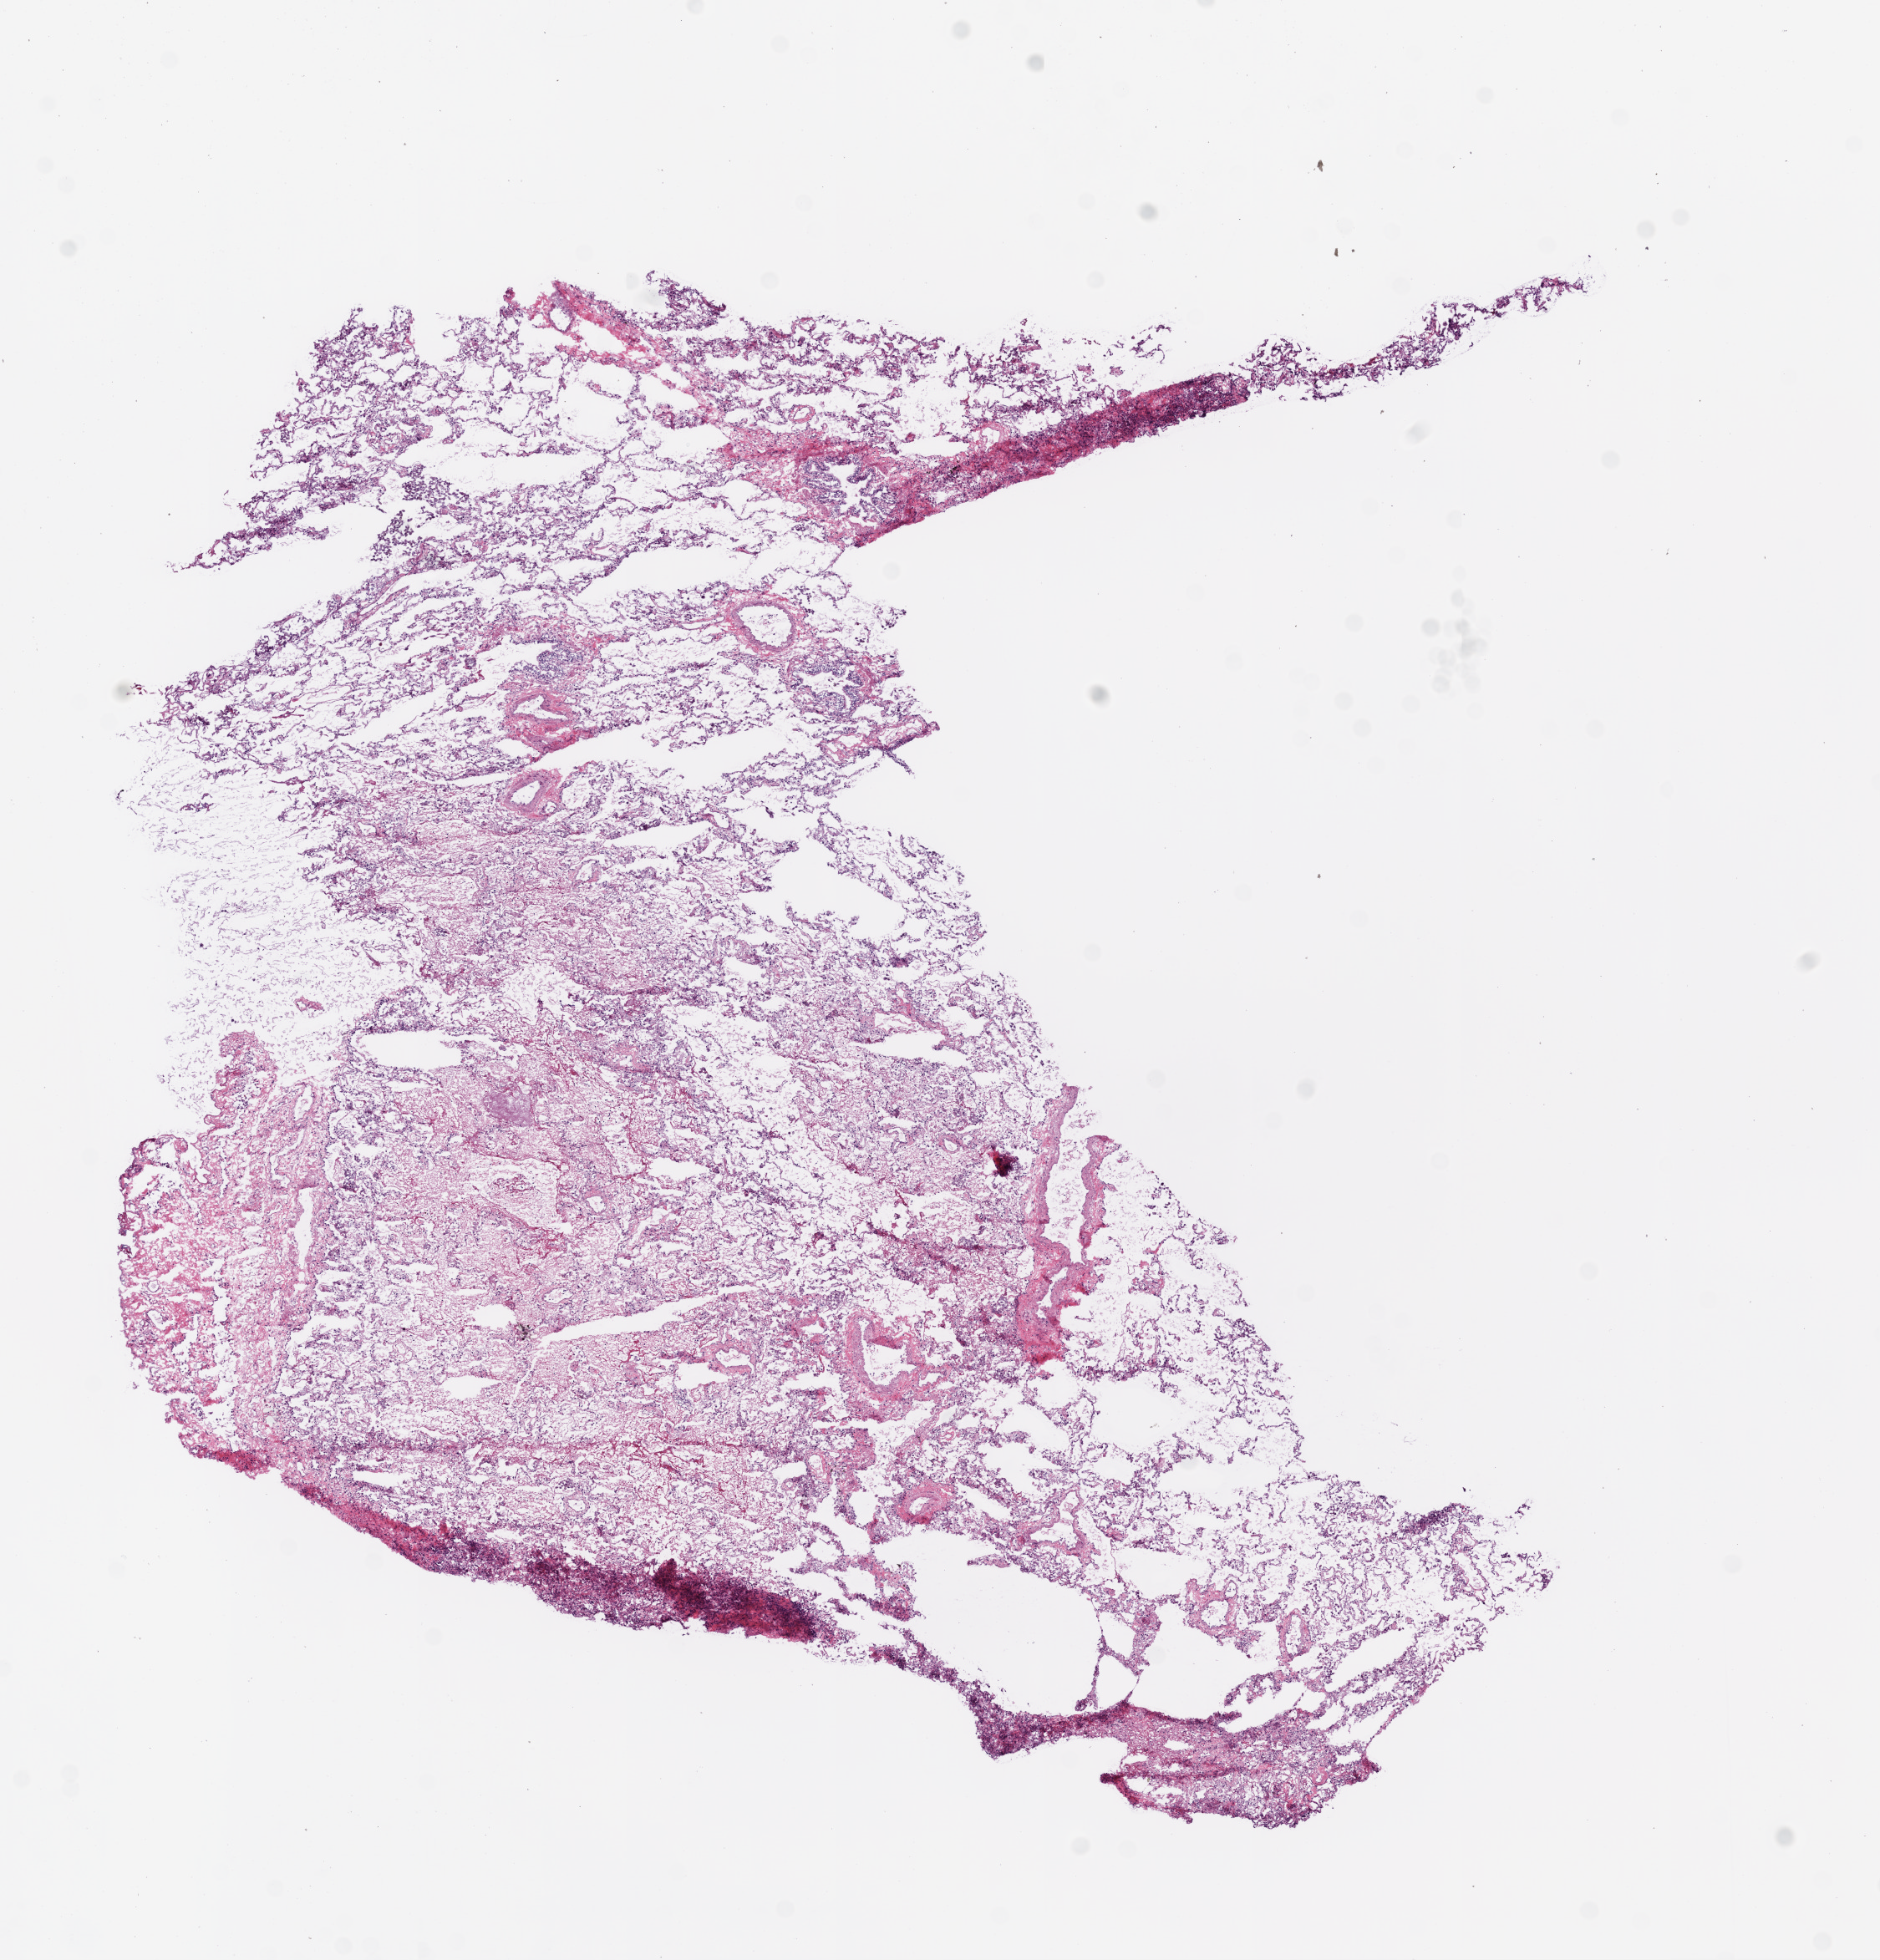
Digitized H&E-stained tissue section (whole slide) — a low-resolution overview of the entire scanned area, about 9.0 x 9.4 mm; frozen section from the bottom of the tissue portion; sample: solid tissue normal (non-tumour tissue), lung. Female, age 66 years at initial diagnosis.
This section: solid tissue normal (non-tumour) sample from the same patient. Patient diagnosis: Squamous cell carcinoma, NOS.